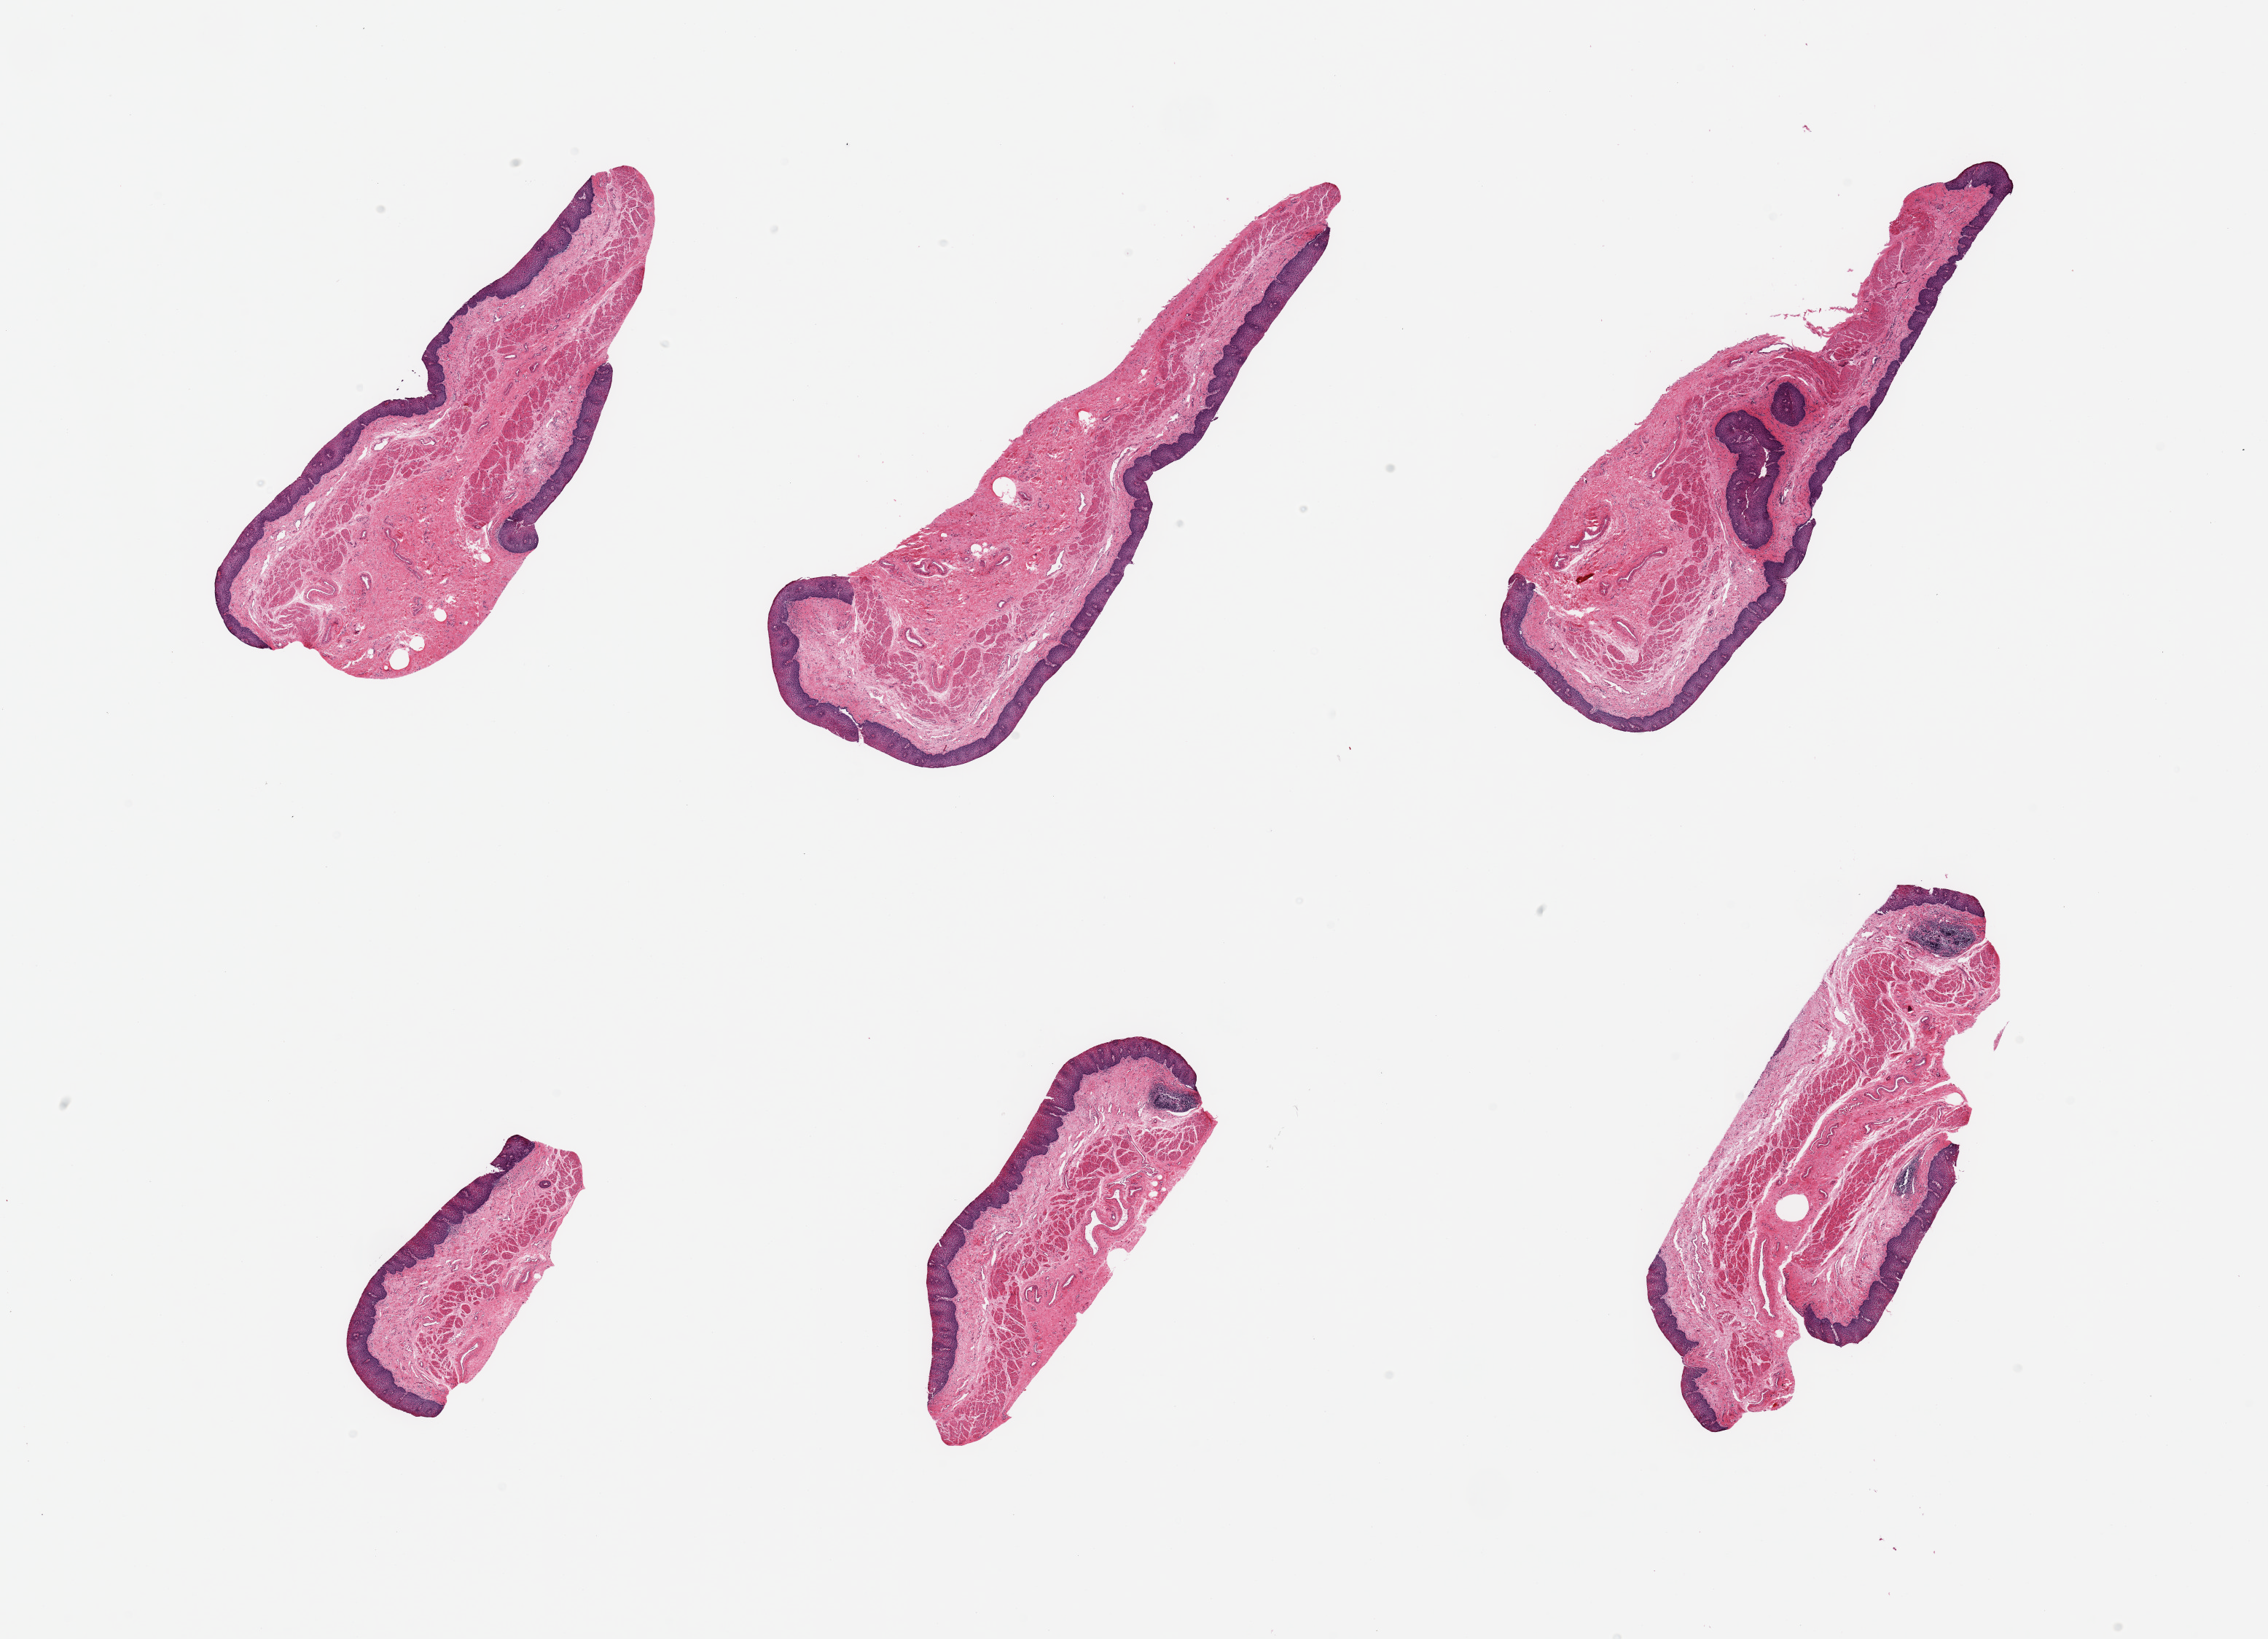
Hematoxylin and eosin (H&E) whole-slide image, whole scanned area (about 24.6 x 17.8 mm) shown as a low-resolution overview. PAXgene-fixed, paraffin-embedded tissue. Section of esophageal mucous membrane (target tissue). Donor tissue sample. Female donor.
Review note (as recorded): 6 pieces; stratified squamous epithelium up to 0.27 mm.